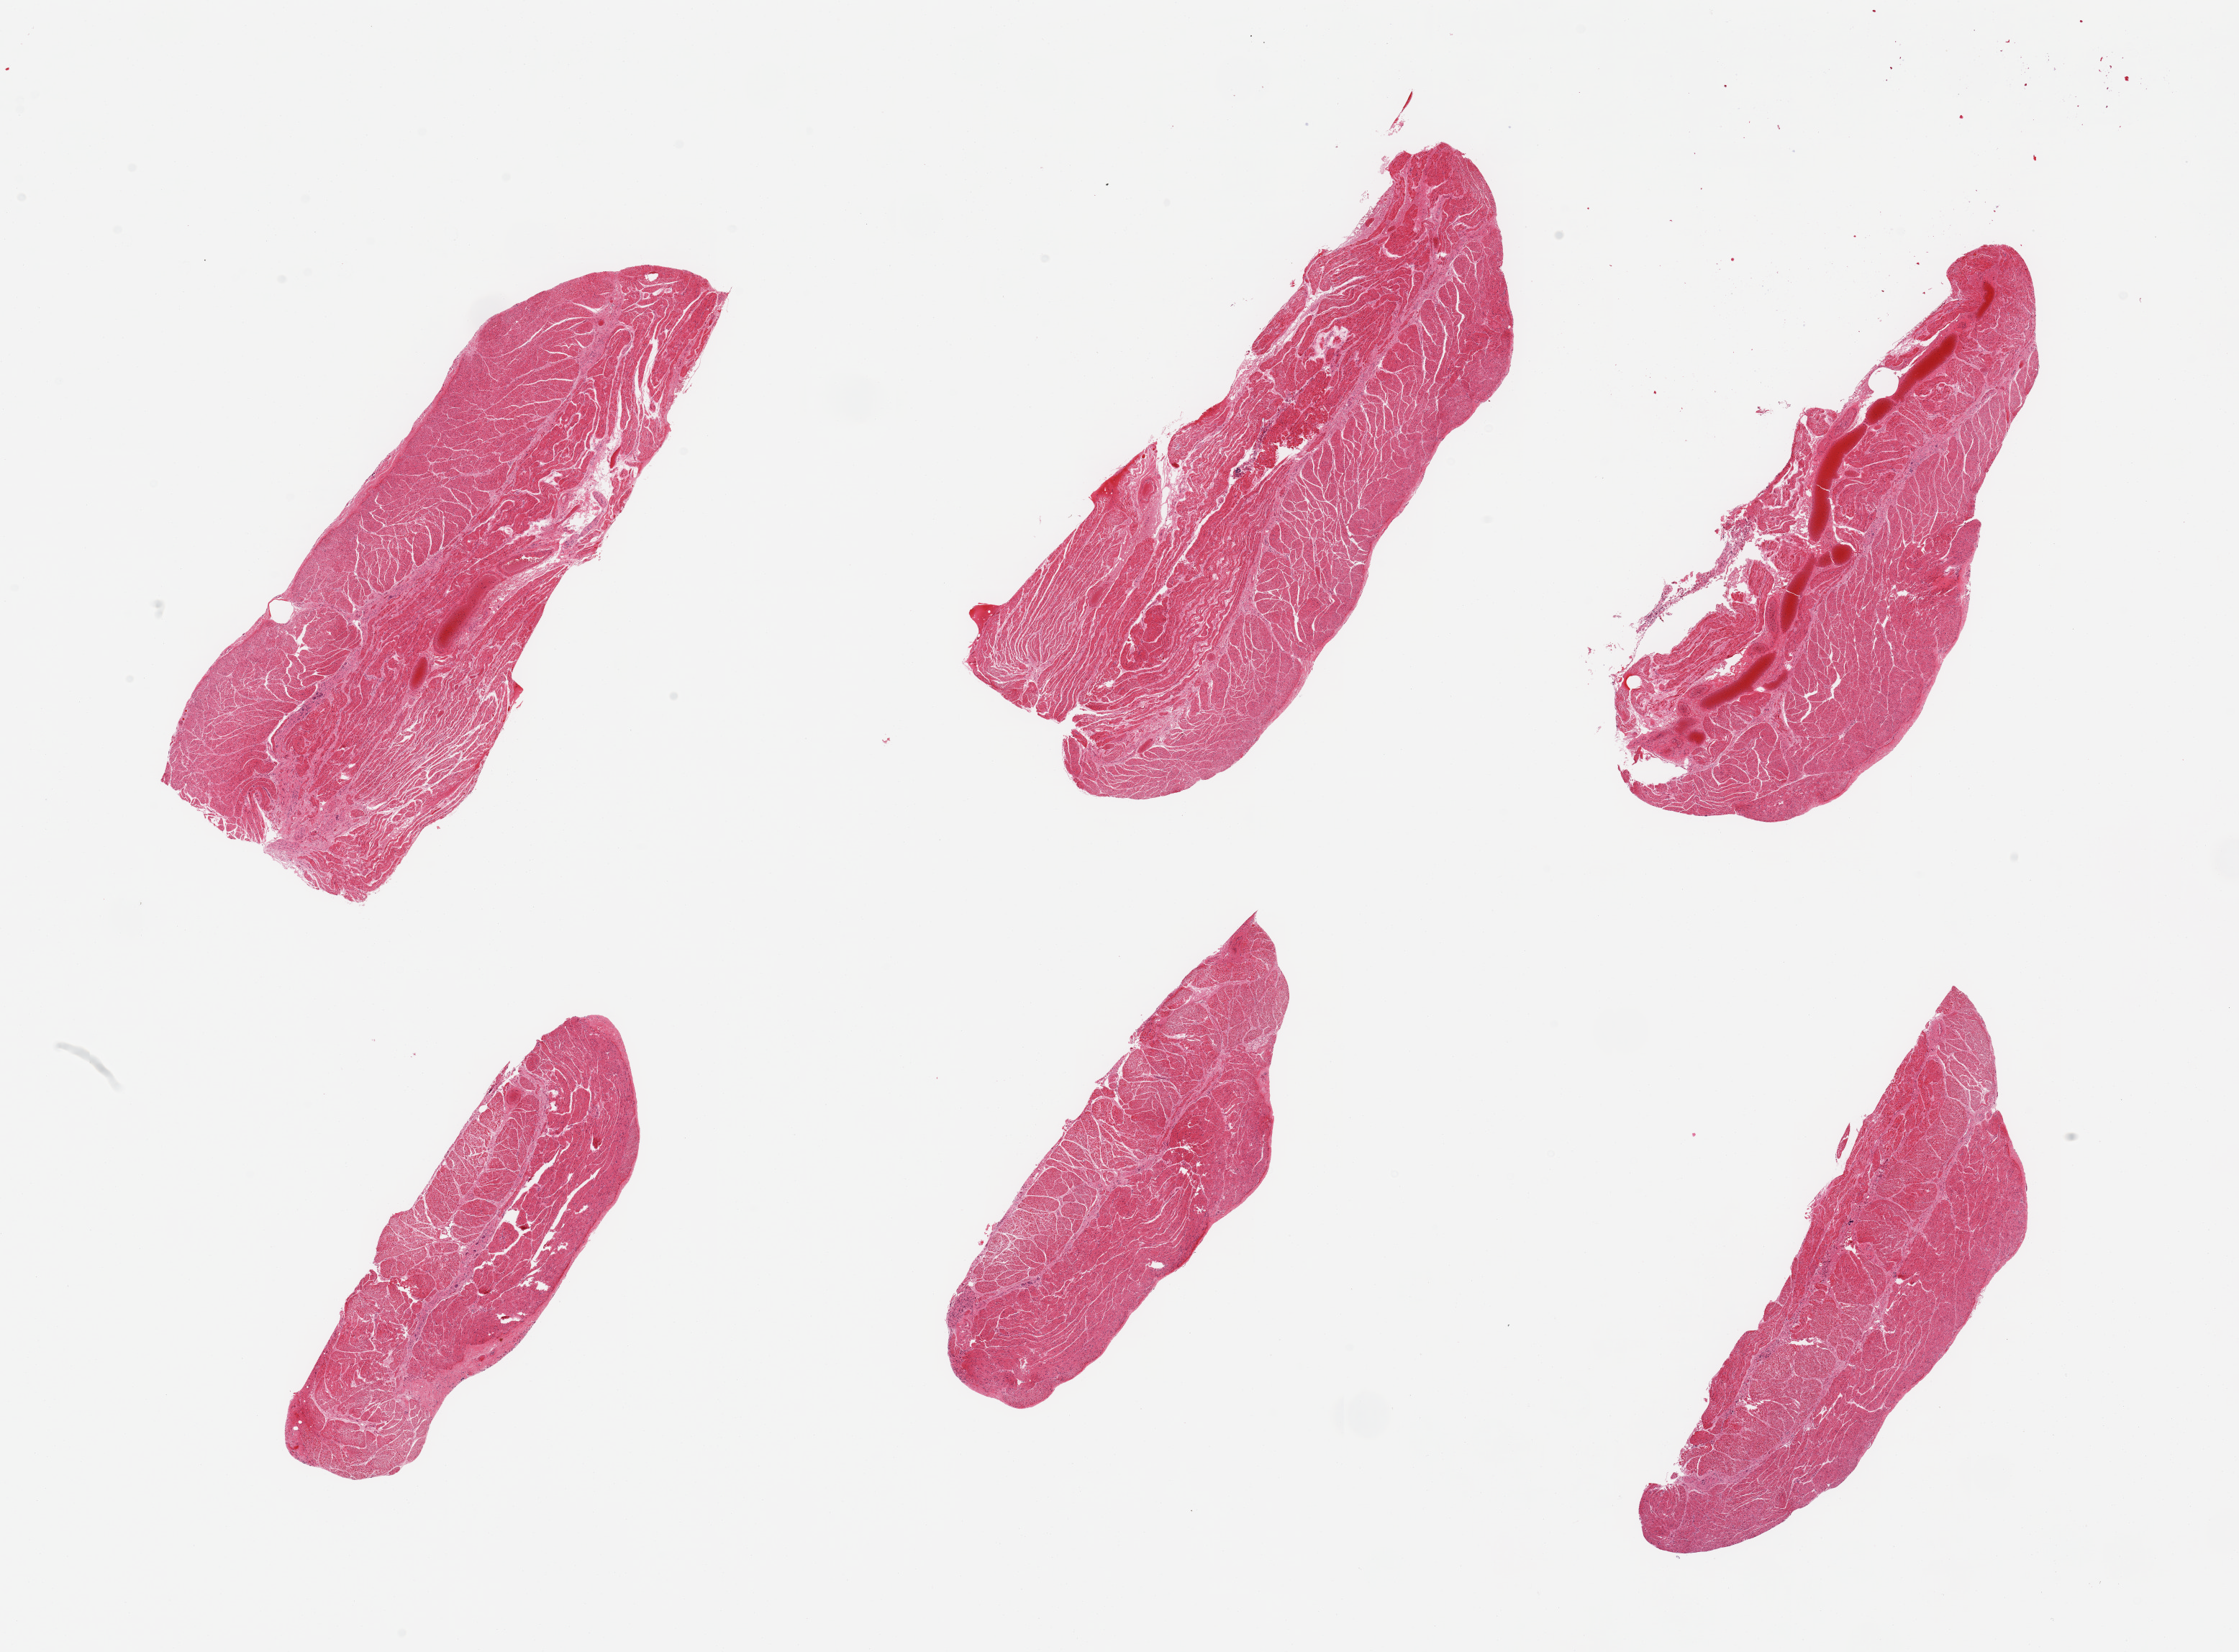
Digitized haematoxylin and eosin-stained section, brightfield — whole scanned area (about 24.6 x 18.2 mm, slide scanned at 20x) shown as a low-resolution overview; PAXgene-fixed paraffin-embedded (PFPE) section; sampled site (target tissue): esophageal muscle; tissue donor sample. Donor: female.
- reviewer comment on this tissue sample: 6 pieces; well dissected muscularis